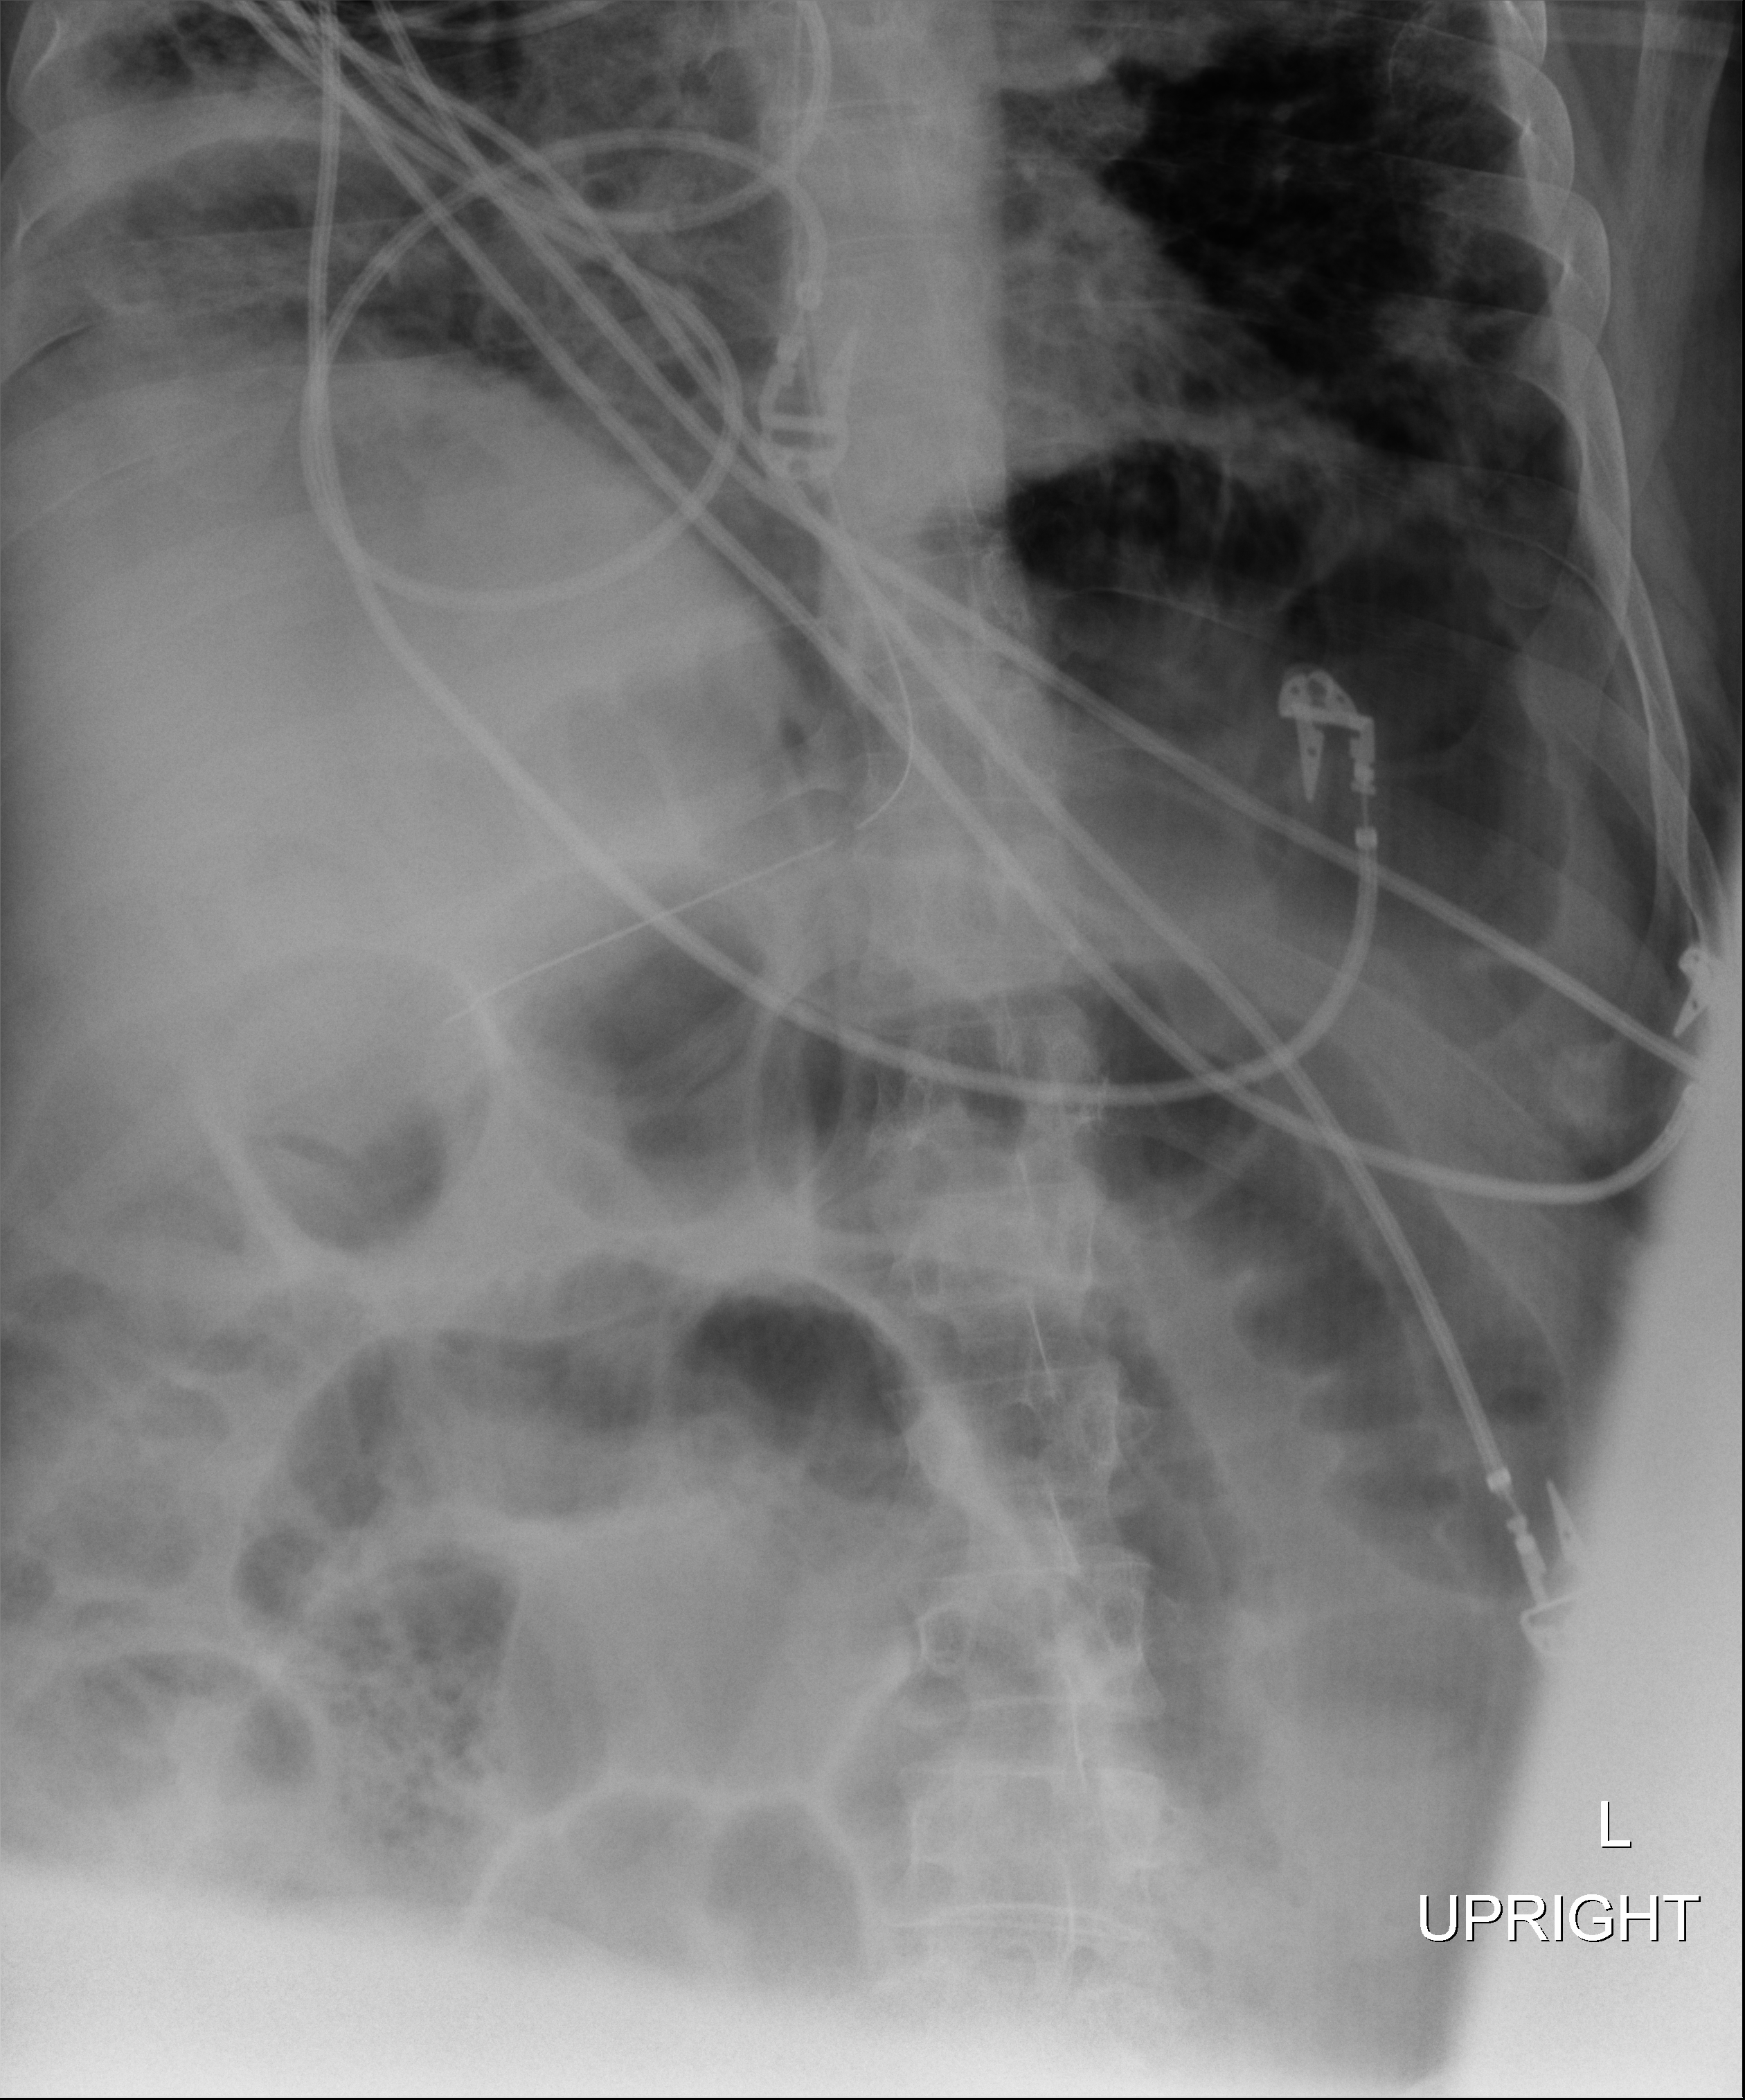
Bedside abdomen radiograph (digital radiography). Patient hospitalised with COVID-19, aged 18–59 years.
From the hospital-stay record, not from the radiograph (when in the stay this image was taken is not recorded):
- mechanically ventilated during this hospital stay: yes
- admitted to intensive care during this hospital stay: yes